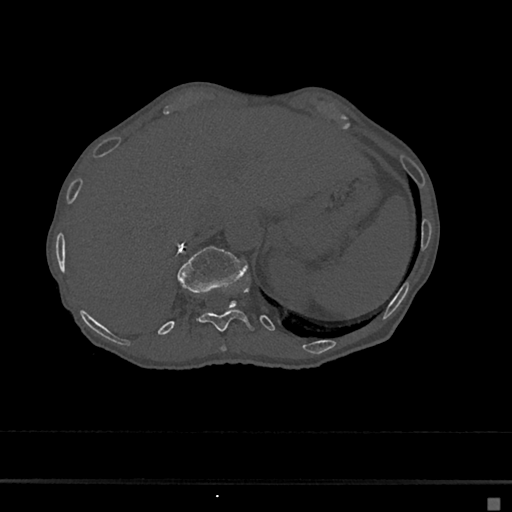
CT including the spine, one axial slice; position 162 of 797 along the scan axis; reconstruction kernel Br40s/3; 120 kVp; bone window (W 1800 / L 400 HU); 0.5 mm slice thickness; 512 × 512 image matrix. Patient: female, 68 years. From the clinical record (not read from this slice): primary cancer: renal.
Structures marked on this image (semi-automatic segmentation, software-assisted and operator-edited):
- T10 vertebra: bounding box <220,345,227,353> (left, top, right, bottom; pixels)
- T11 vertebra: <196,286,255,331>
- T12 vertebra: <177,246,248,308>